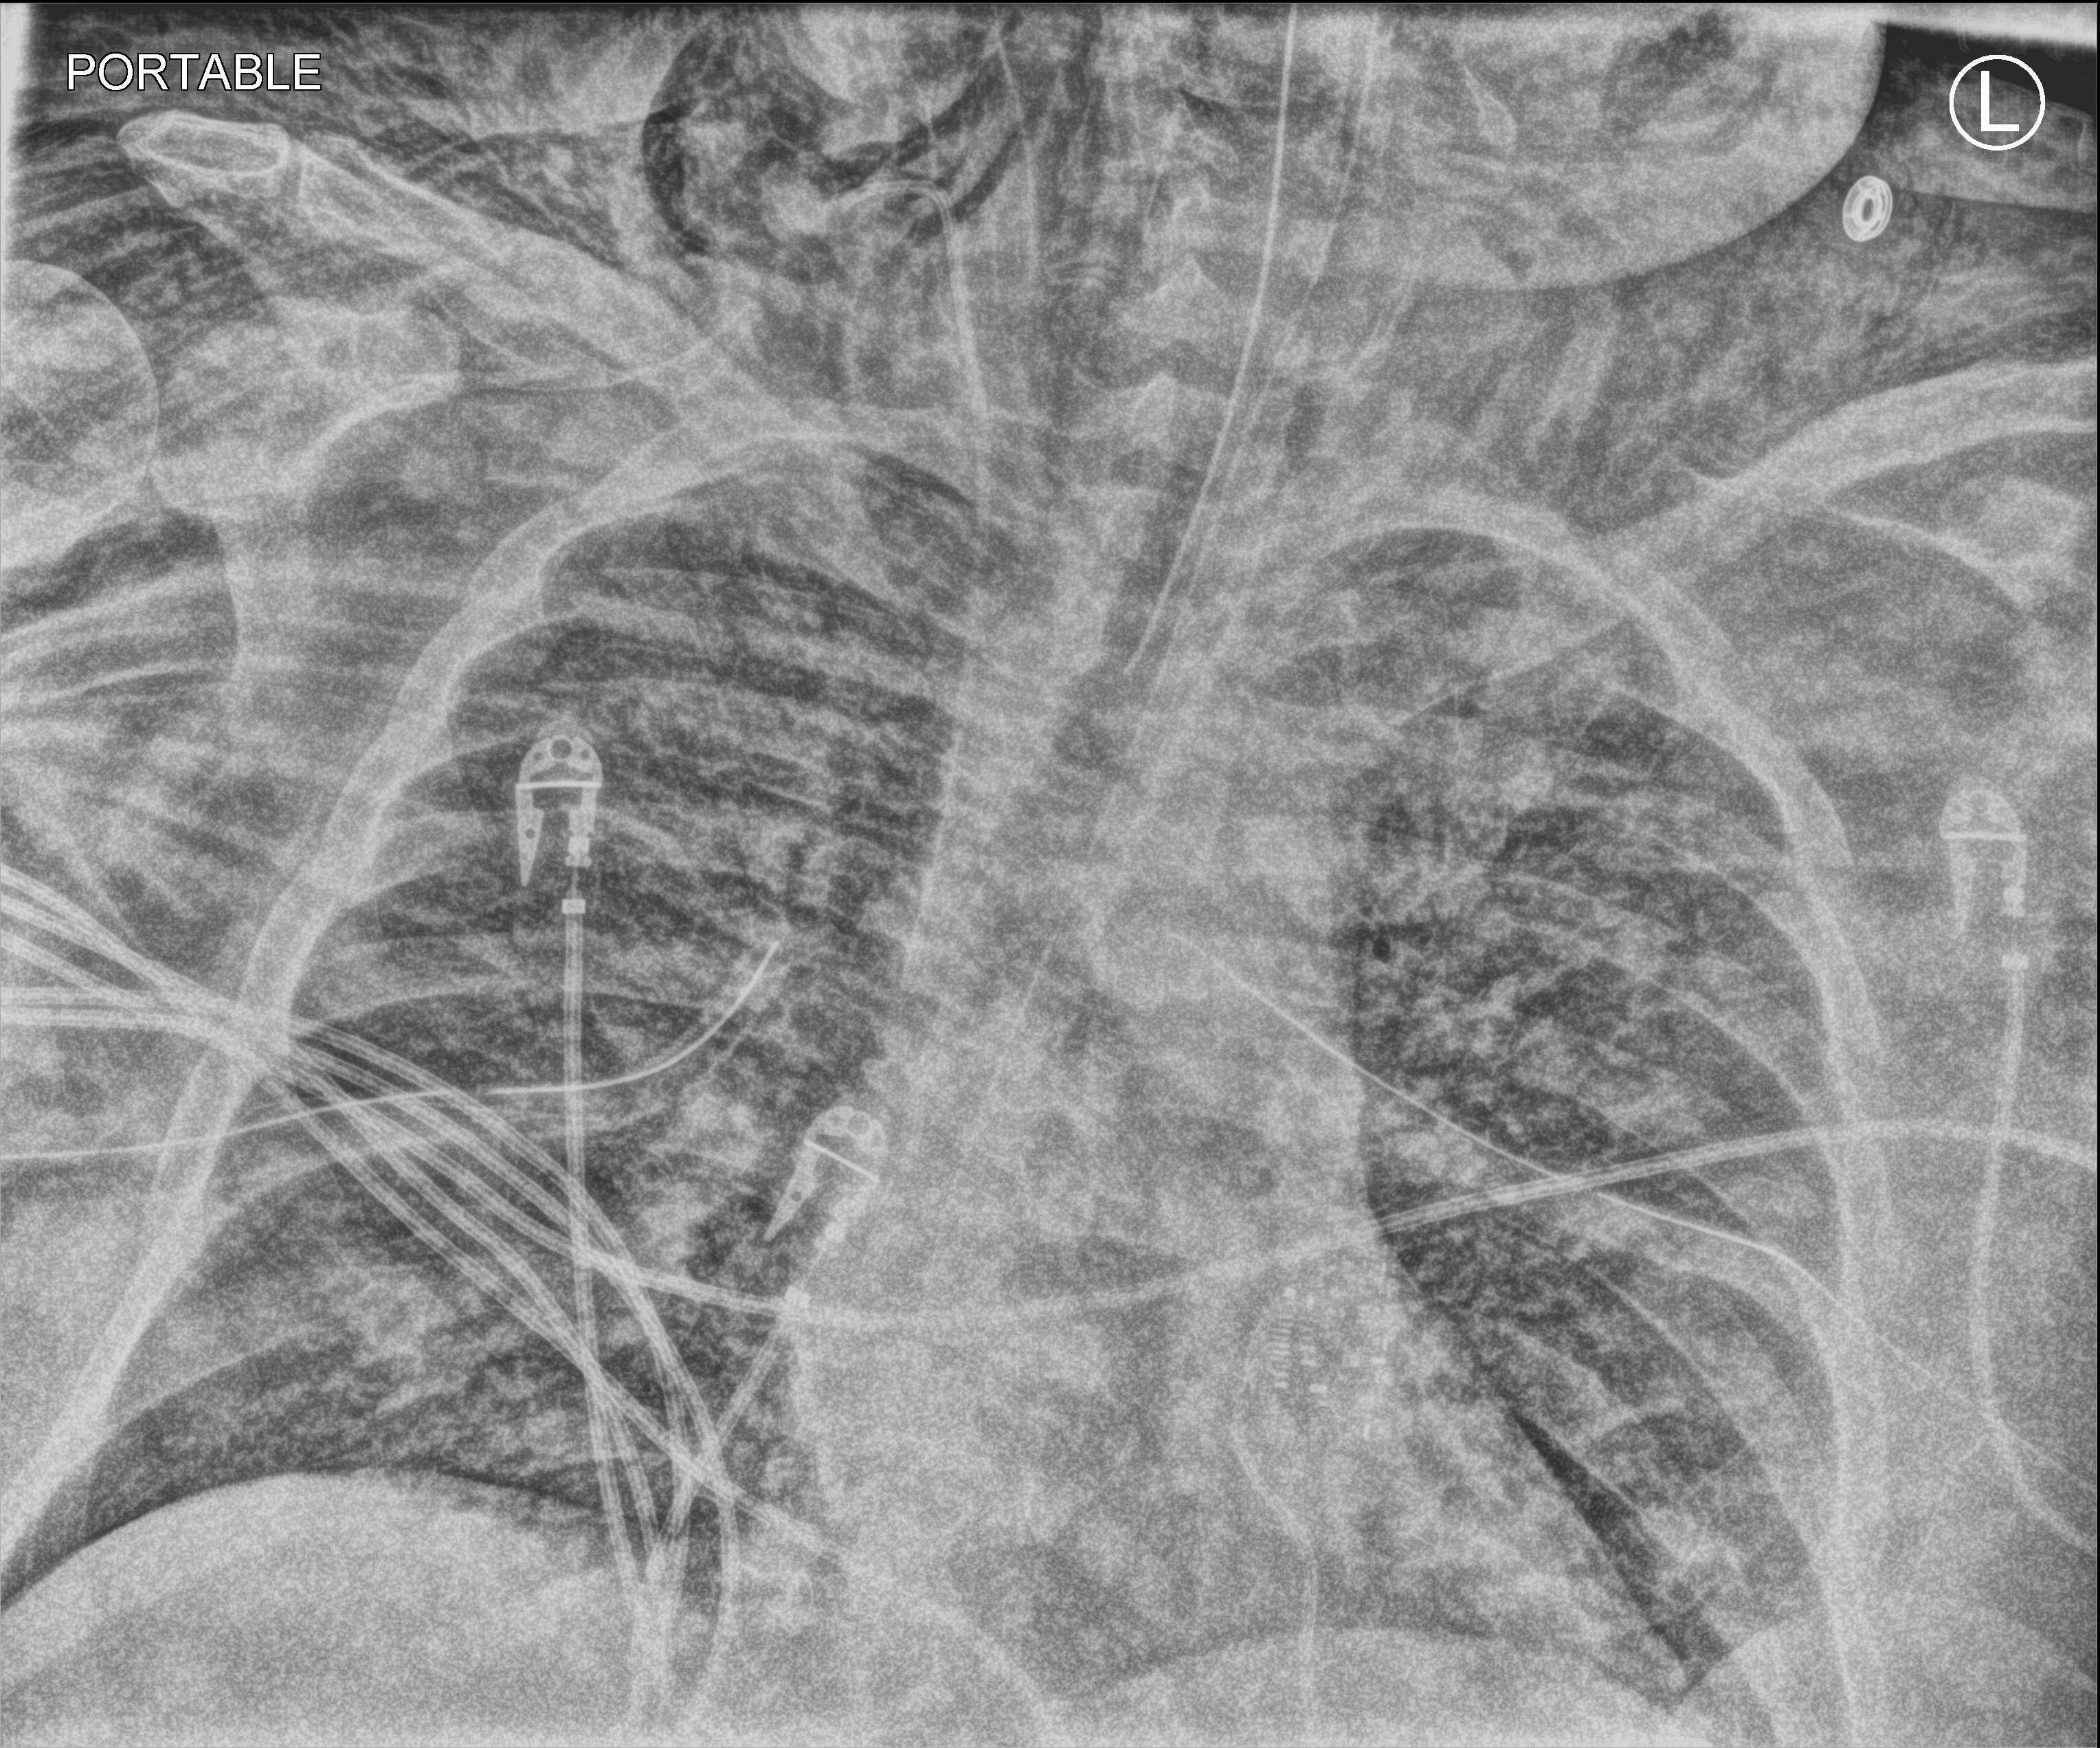
Bedside chest radiograph (computed radiography). Patient hospitalised with COVID-19, aged 18–59 years.
From the hospital-stay record, not from the radiograph (when in the stay this image was taken is not recorded):
- length of hospital stay: 26 days
- smoking status (admission record): never